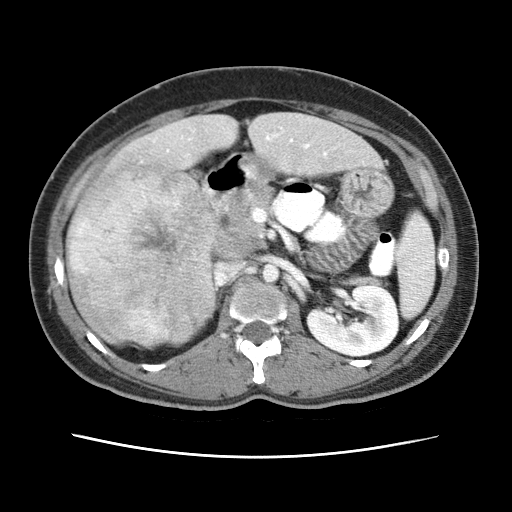
Contrast-enhanced abdominal CT (liver protocol), one axial slice; slice 21 of 79 in the series (ordered by position); reconstruction kernel STANDARD; 120 kVp; soft-tissue window (W 400 / L 40 HU); 2.5 mm slice thickness; 512 × 512 image matrix. From the clinical record (not read from this slice): diagnosis: hepatocellular carcinoma (patient treated with transarterial chemoembolisation; whether this scan precedes or follows treatment is not stated here); TNM stage (as recorded): Stage-I; Child-Pugh class: A.
Outlined on this slice (semi-automatic segmentation, software-assisted and operator-edited):
- abdominal aorta: bounding box (x1, y1, x2, y2) in pixels: (262, 264, 280, 282)
- liver parenchyma outside the tumour (the mass and vessels are separate outlines, so this box may not span the whole liver): (66, 112, 380, 346)
- mass: (67, 159, 223, 347)
- liver vessels: (167, 127, 327, 156)